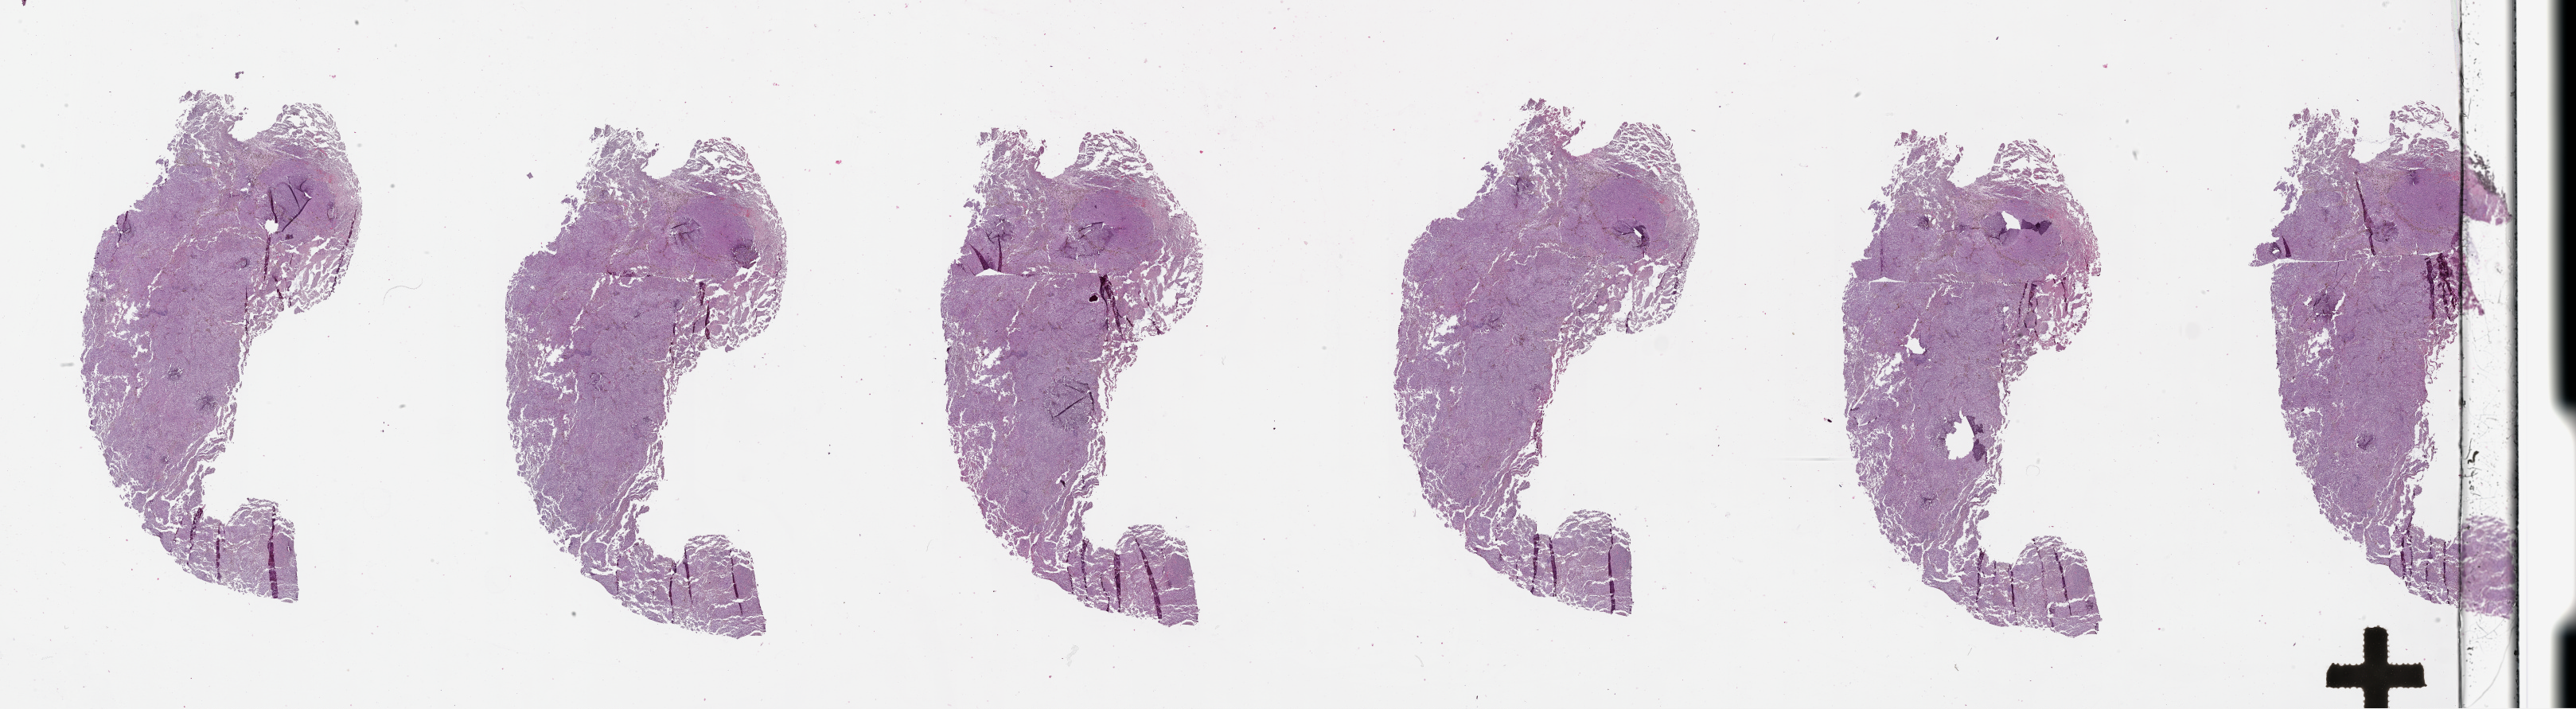
H&E whole-slide image, low-resolution overview of the scanned area, about 52.1 x 14.3 mm. Female, 70 y/o.
• patient diagnosis: Malignant melanoma, NOS